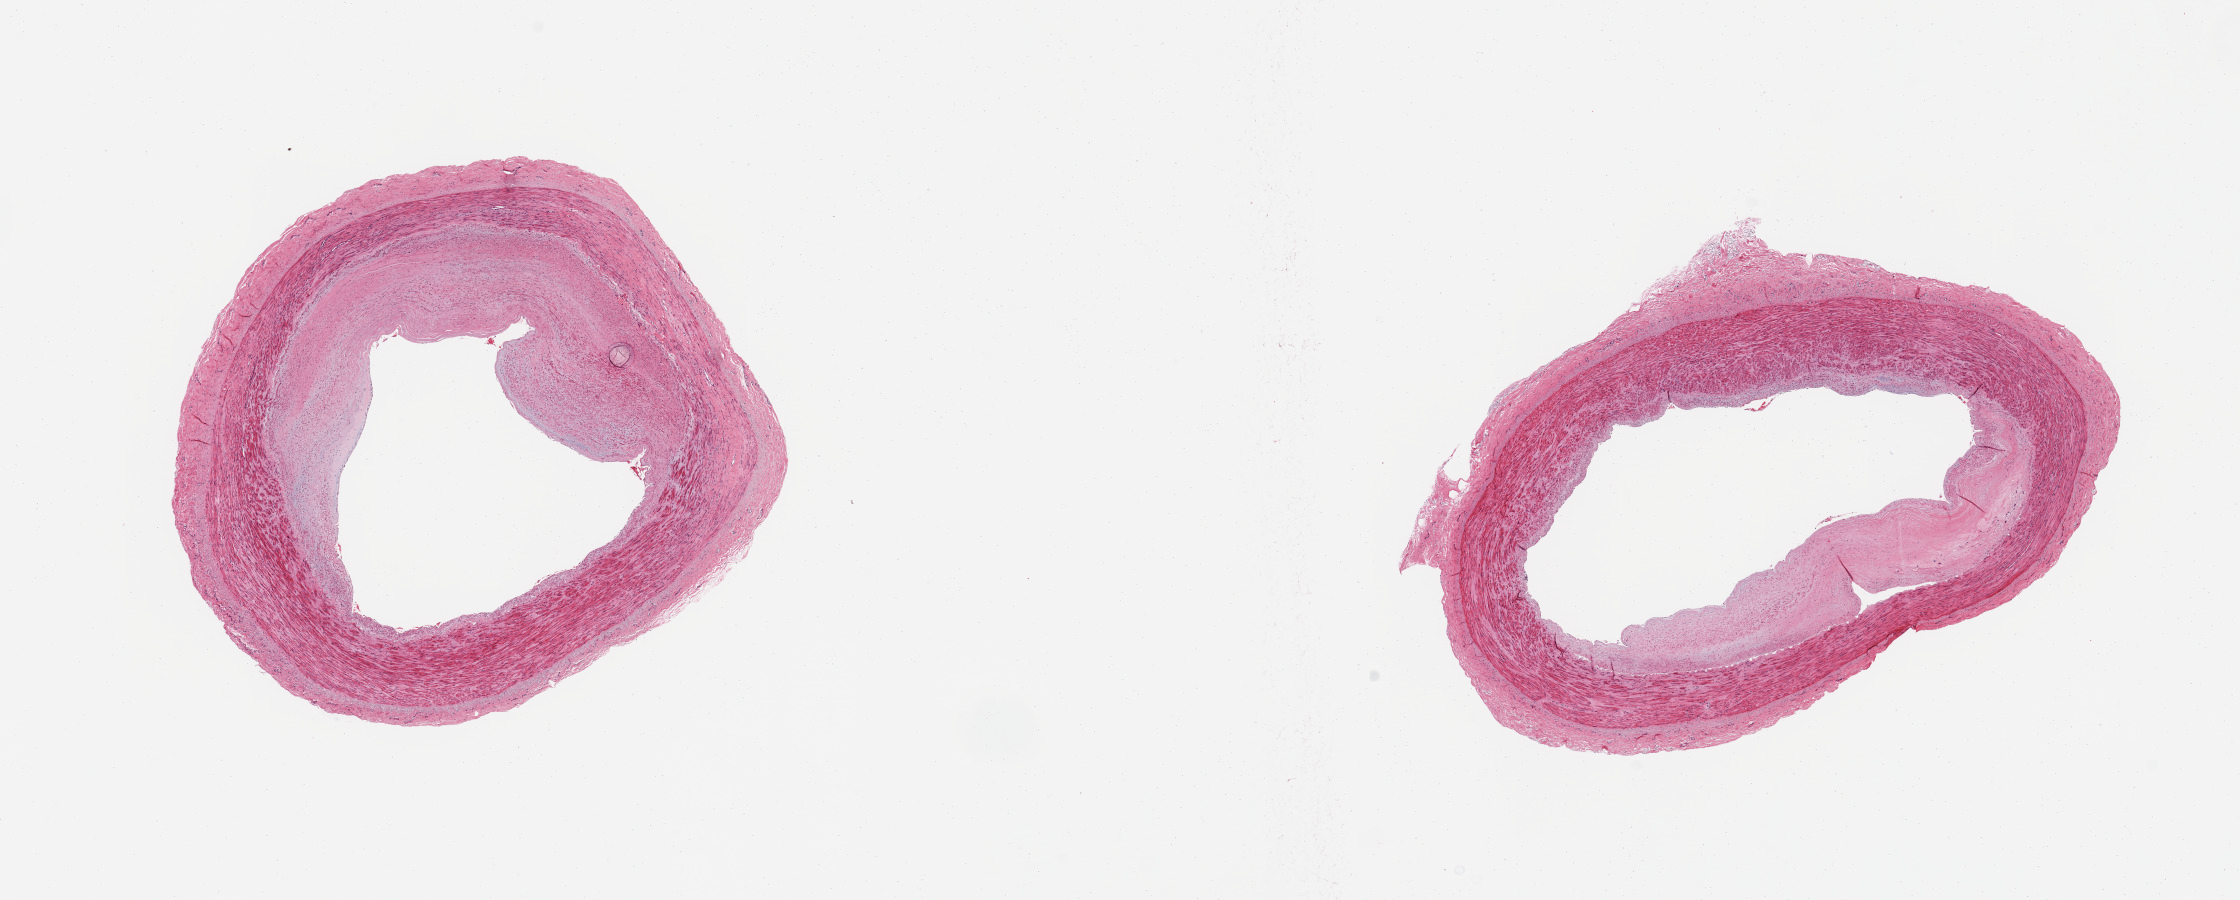
H&E whole-slide image, brightfield, shown as a low-resolution overview of the whole scanned area (about 17.7 x 7.1 mm); PAXgene-fixed paraffin-embedded (PFPE) section; target tissue: tibial artery; tissue donor sample. Donor sex: male.
Review note (as recorded): 2 pieces, ~40% occlusive atherosis, no adherent fat.